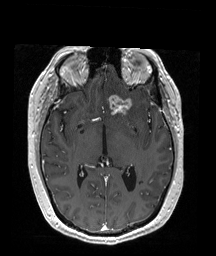
Brain MRI from a brain-tumour surgery series, one axial slice; position 102 of 192 along the scan axis; T1-weighted post-contrast; 1 mm slice thickness; 216 × 256 image matrix, field of view 211 × 250 mm. From the clinical record (not read from this slice): histopathology: Oligodendroglioma; WHO grade: 2; IDH mutation: yes.
Outlined on this slice (expert manual segmentation):
- tumour: bounding box <107,95,132,117> (left, top, right, bottom; pixels)